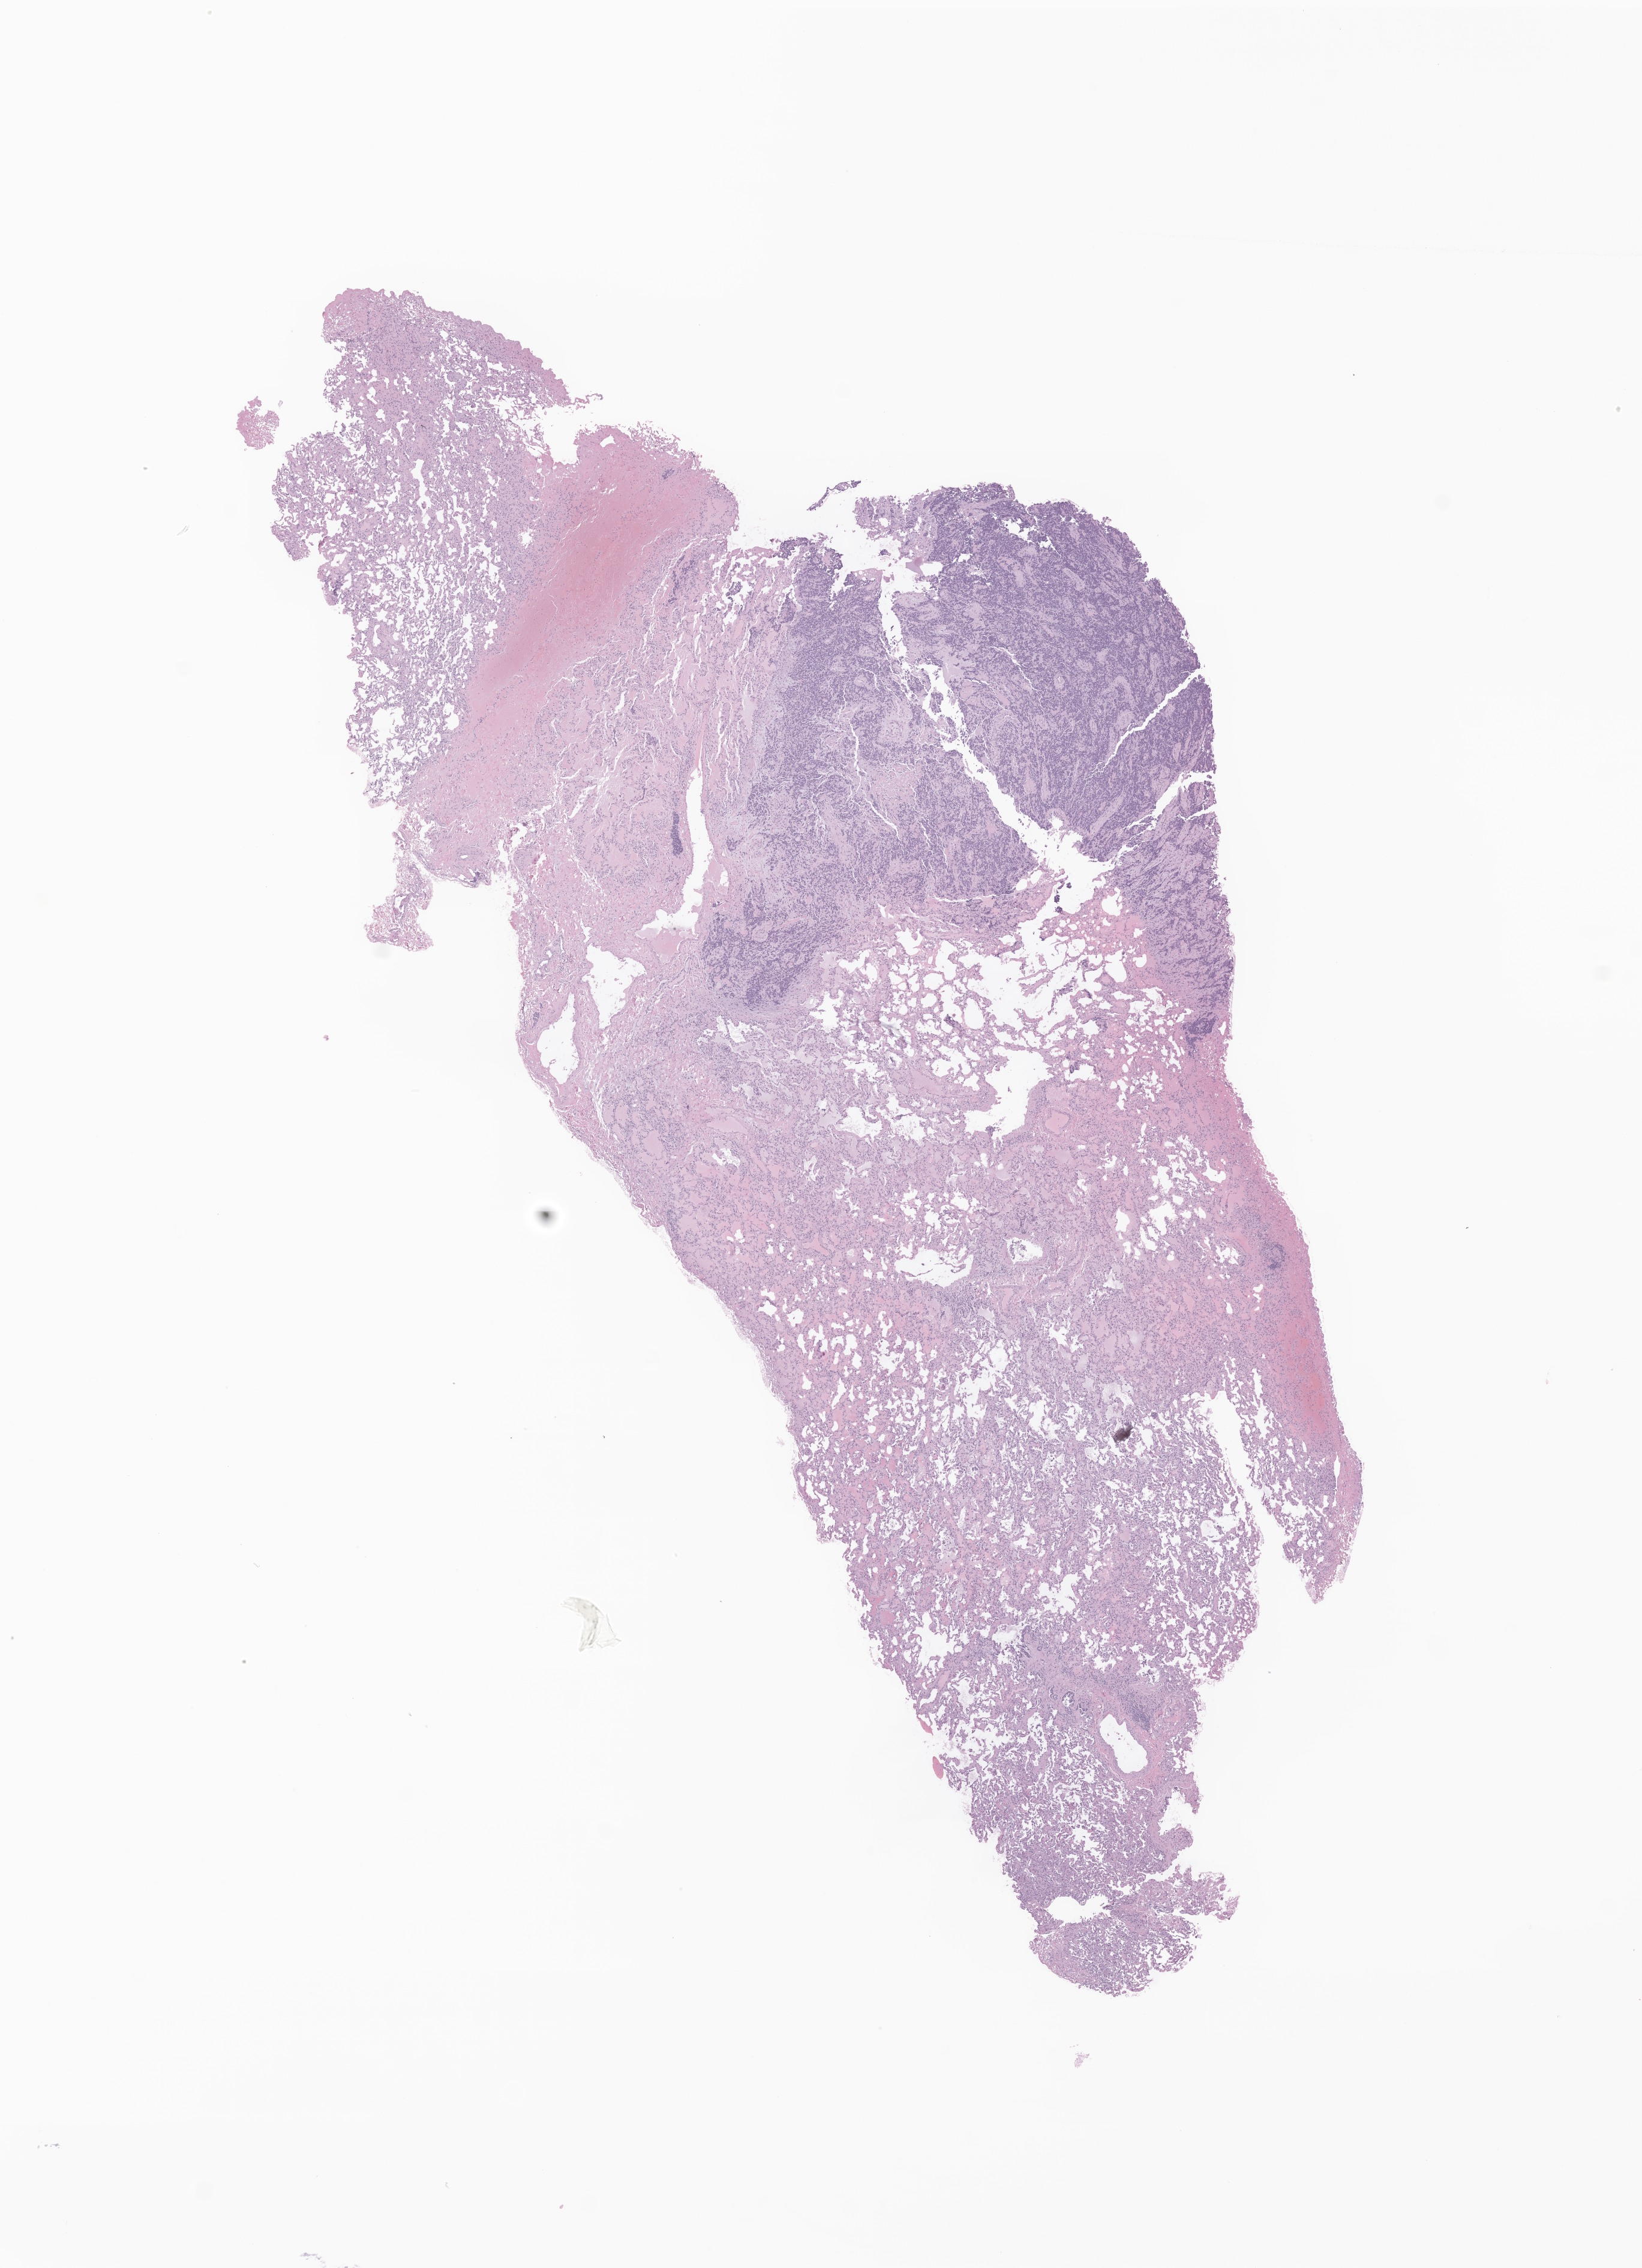
Digitized haematoxylin and eosin-stained section of tumor tissue from the renal pelvis — a low-resolution overview of the entire scanned area, about 11.5 x 15.9 mm; formalin-fixed, paraffin-embedded (FFPE) tissue. Female patient, age 143 months (11 years 11 months).
Diagnosis (ICD-O-3 morphology term): Renal cell carcinoma, NOS.